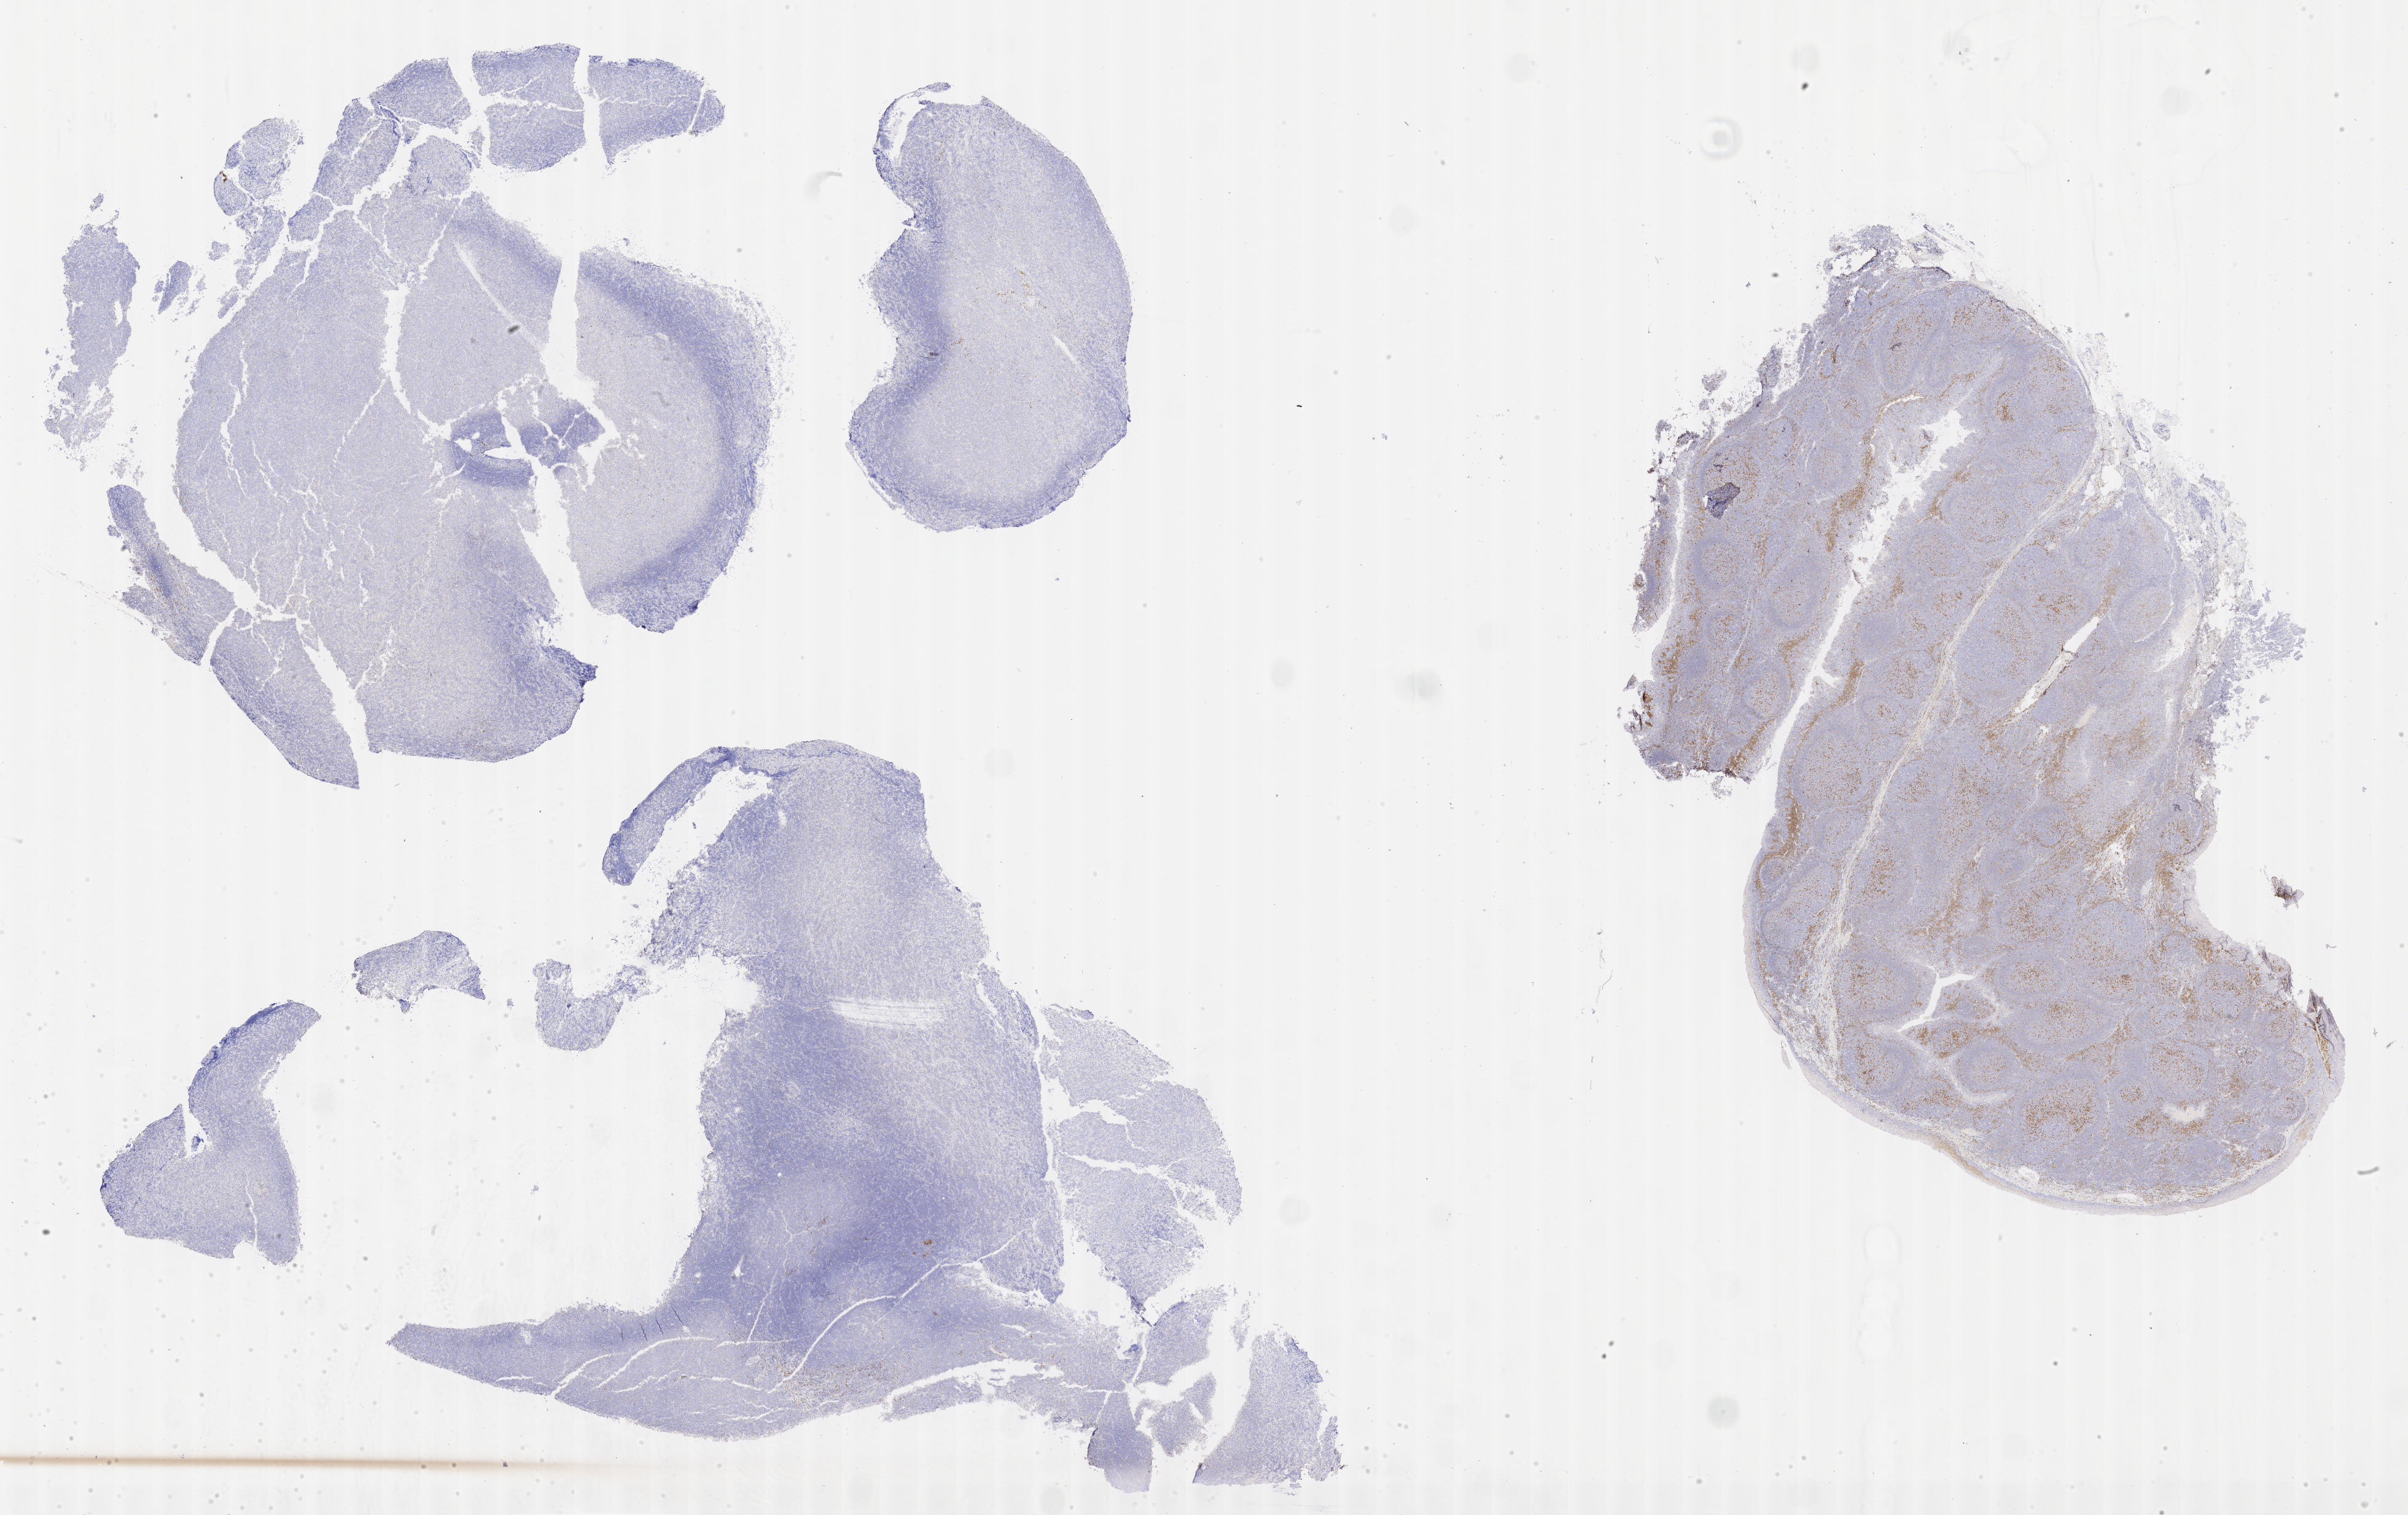
IHC for IRF4/MUM1, whole-slide image — whole scanned area (about 31.7 x 19.9 mm) shown as a low-resolution overview; tumor tissue; site: liver. Patient: male, aged 45.
Histologic diagnosis: Diffuse large B-cell lymphoma, NOS.